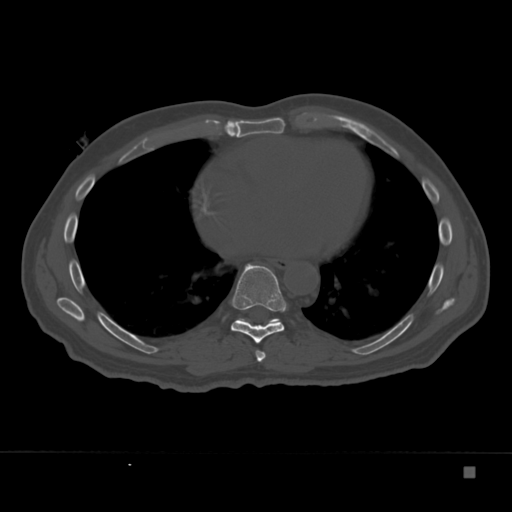
CT including the spine, one axial slice; reconstruction kernel Br40s; bone window (W 1800 / L 400 HU); 1.5 mm slice thickness; 512 × 512 image matrix, field of view 389 × 389 mm. Male patient, age 72 years. Case-level facts recorded for this patient, not image findings: primary cancer: skeletal.
Structures marked on this image (semi-automatic segmentation, software-assisted and operator-edited):
- T7 vertebra: bounding box <255,350,266,362> (left, top, right, bottom; pixels)
- T8 vertebra: <231,263,287,344>
- T9 vertebra: <238,318,280,326>